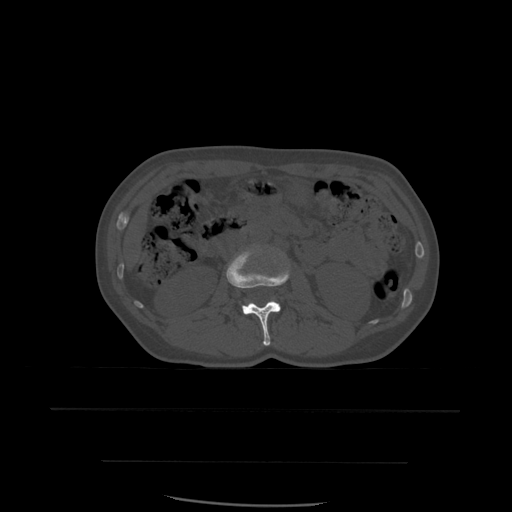
CT including the spine, one axial slice. Position 219 of 574 along the scan axis. Bone window (W 1800 / L 400 HU). 1.25 mm slice thickness. 512 × 512 image matrix, field of view 392 × 392 mm. Patient age 48 years. Case-level facts recorded for this patient, not image findings: primary cancer: lung.
Annotated regions visible in this slice (semi-automatic segmentation, software-assisted and operator-edited):
- L2 vertebra: box from (x=227, y=249) to (x=290, y=346) px